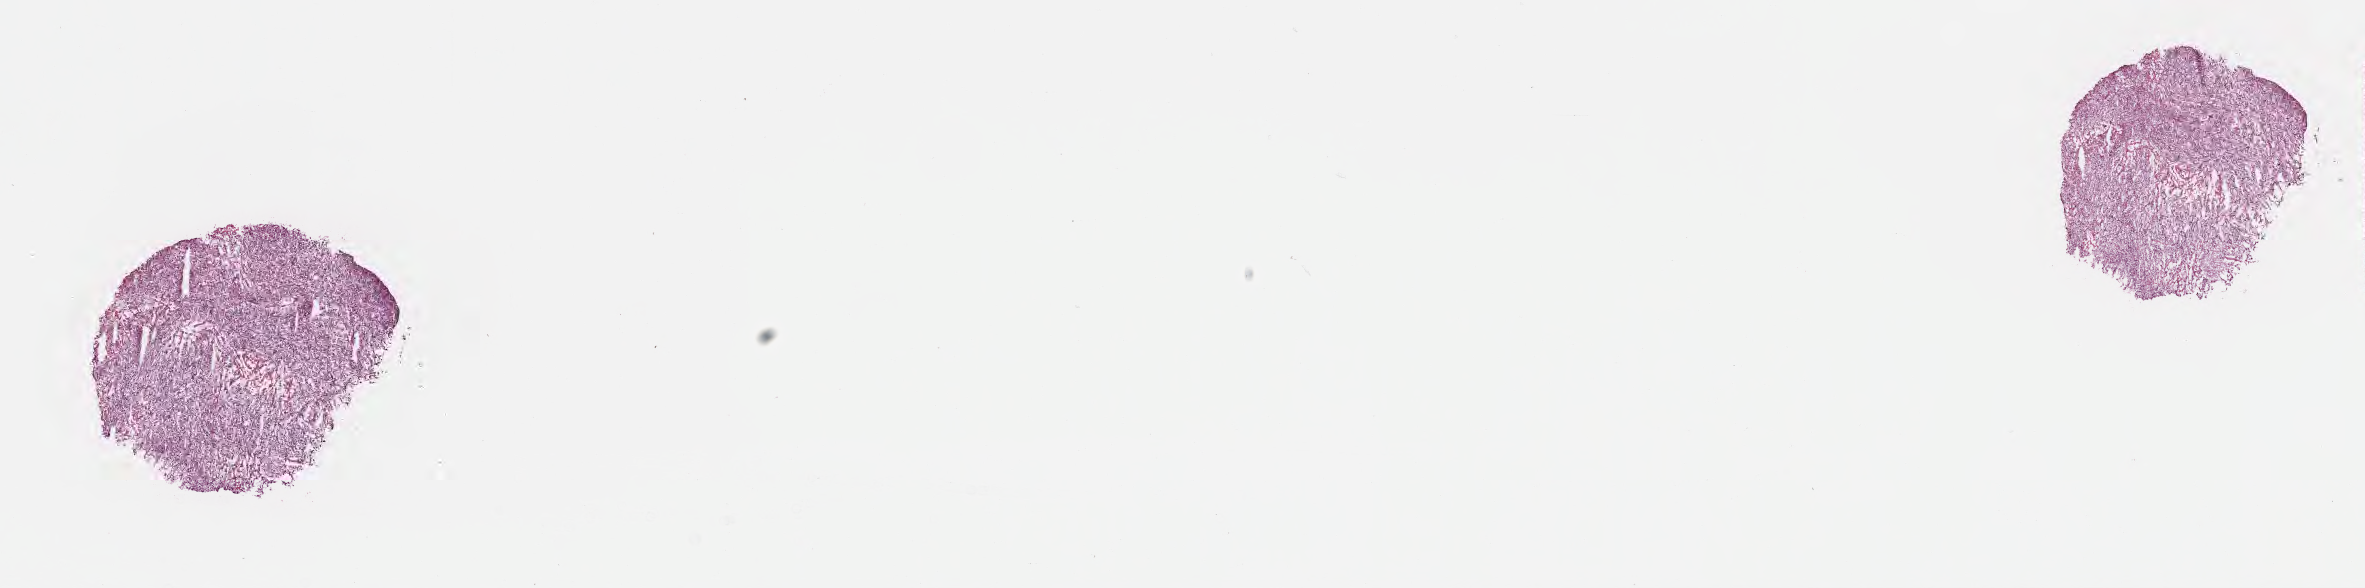
Digitized hematoxylin and eosin (H&E)-stained section — shown as a low-resolution overview of the whole scanned area (about 19.1 x 4.8 mm), frozen section (tissue freezing medium), metastatic tumor tissue, resected from brain. Patient: female, age at initial diagnosis 55 years. Slide review estimates, as recorded: tumor cells 79%, tumor nuclei 95%, stromal cells 15%, necrosis 6%, normal cells 0%. Infiltration values recorded for this section: lymphocyte infiltration 3%, monocyte infiltration 0%, neutrophil infiltration 0%.
Patient diagnosis (primary): Malignant melanoma, NOS.